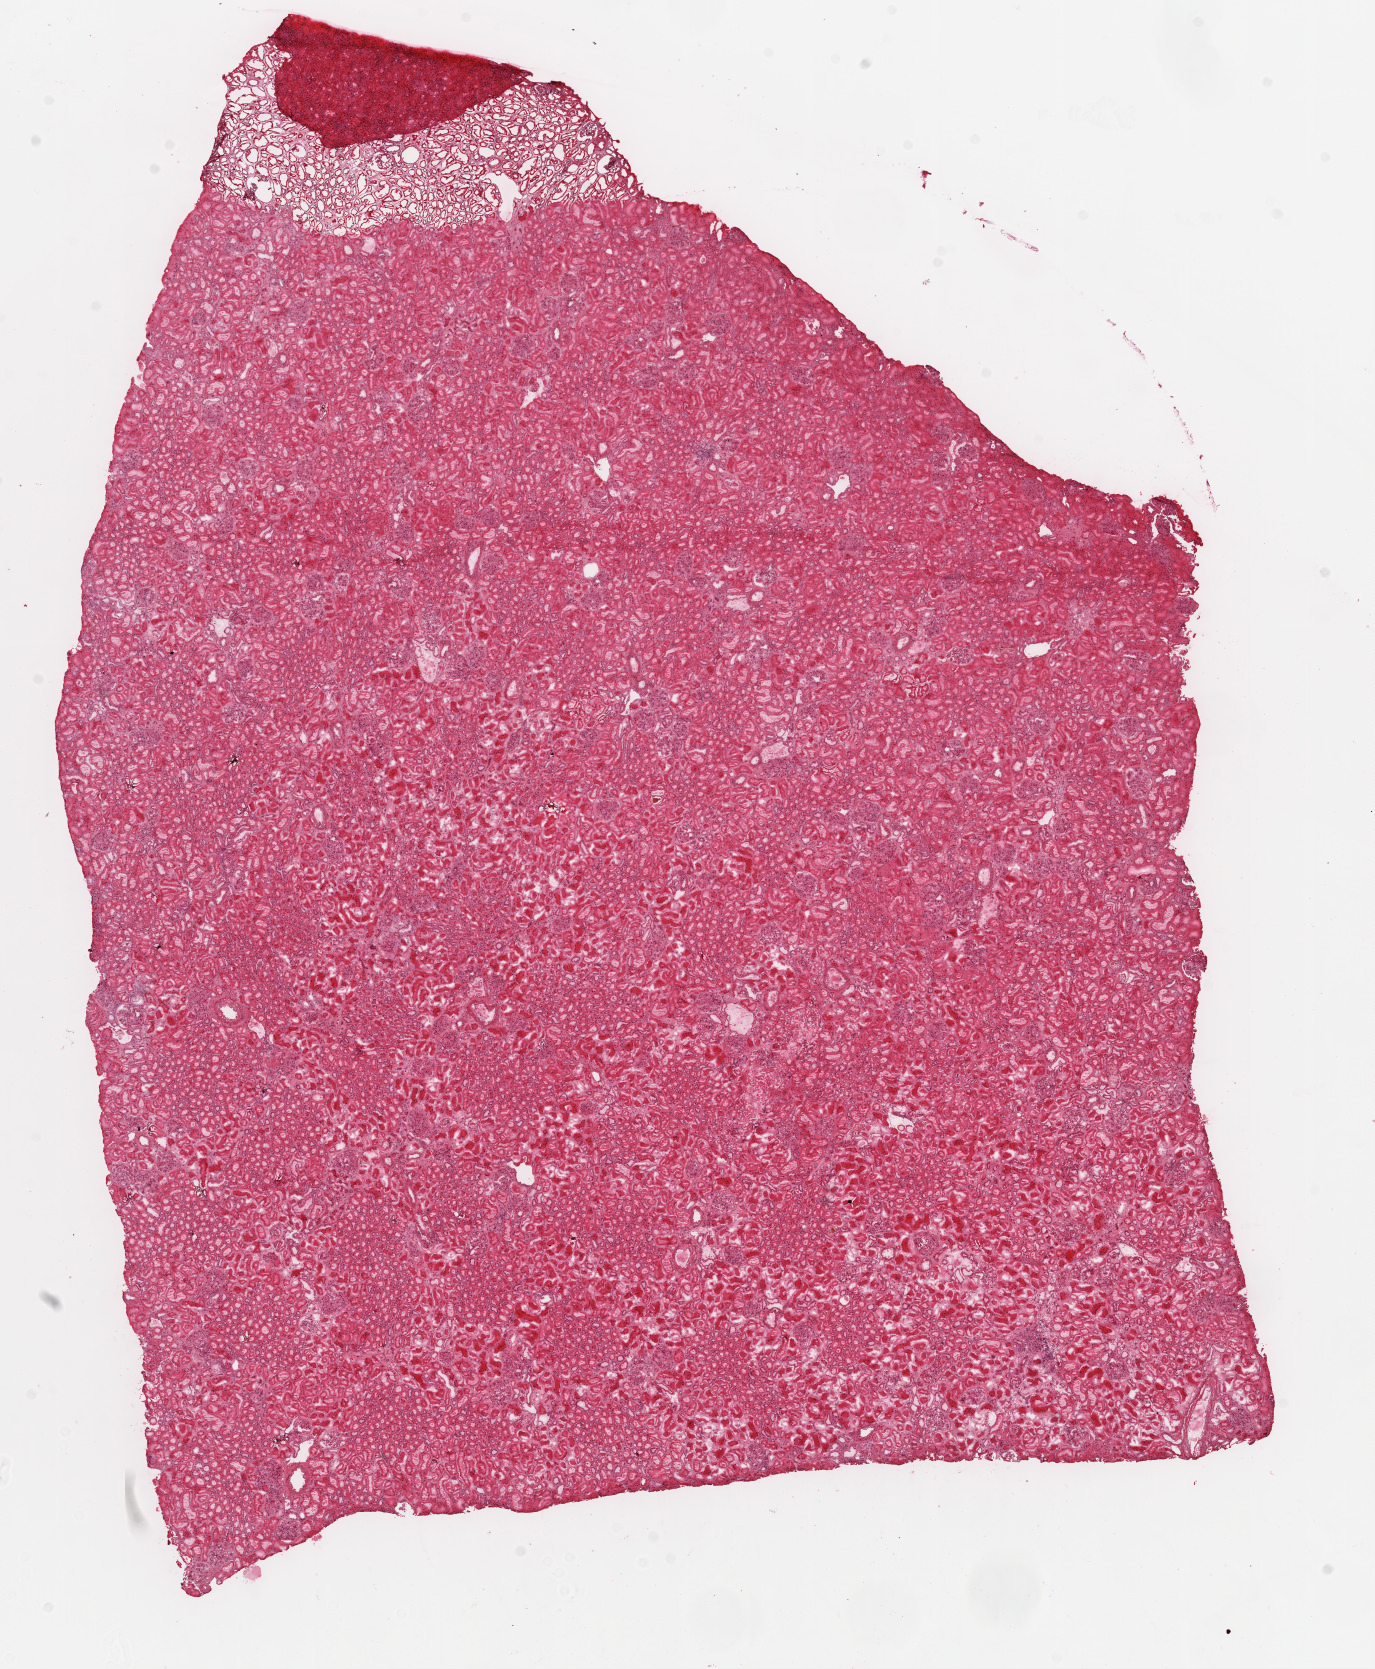
Digitized H&E-stained tissue section (whole slide), whole scanned area (about 11.0 x 13.4 mm) shown as a low-resolution overview; frozen section from the top of the tissue portion; kidney, solid tissue normal (non-tumour tissue) sample. Male patient; age at initial diagnosis 68 years.
* this section: solid tissue normal sample (biorepository sample class)
* patient diagnosis: Clear cell adenocarcinoma, NOS